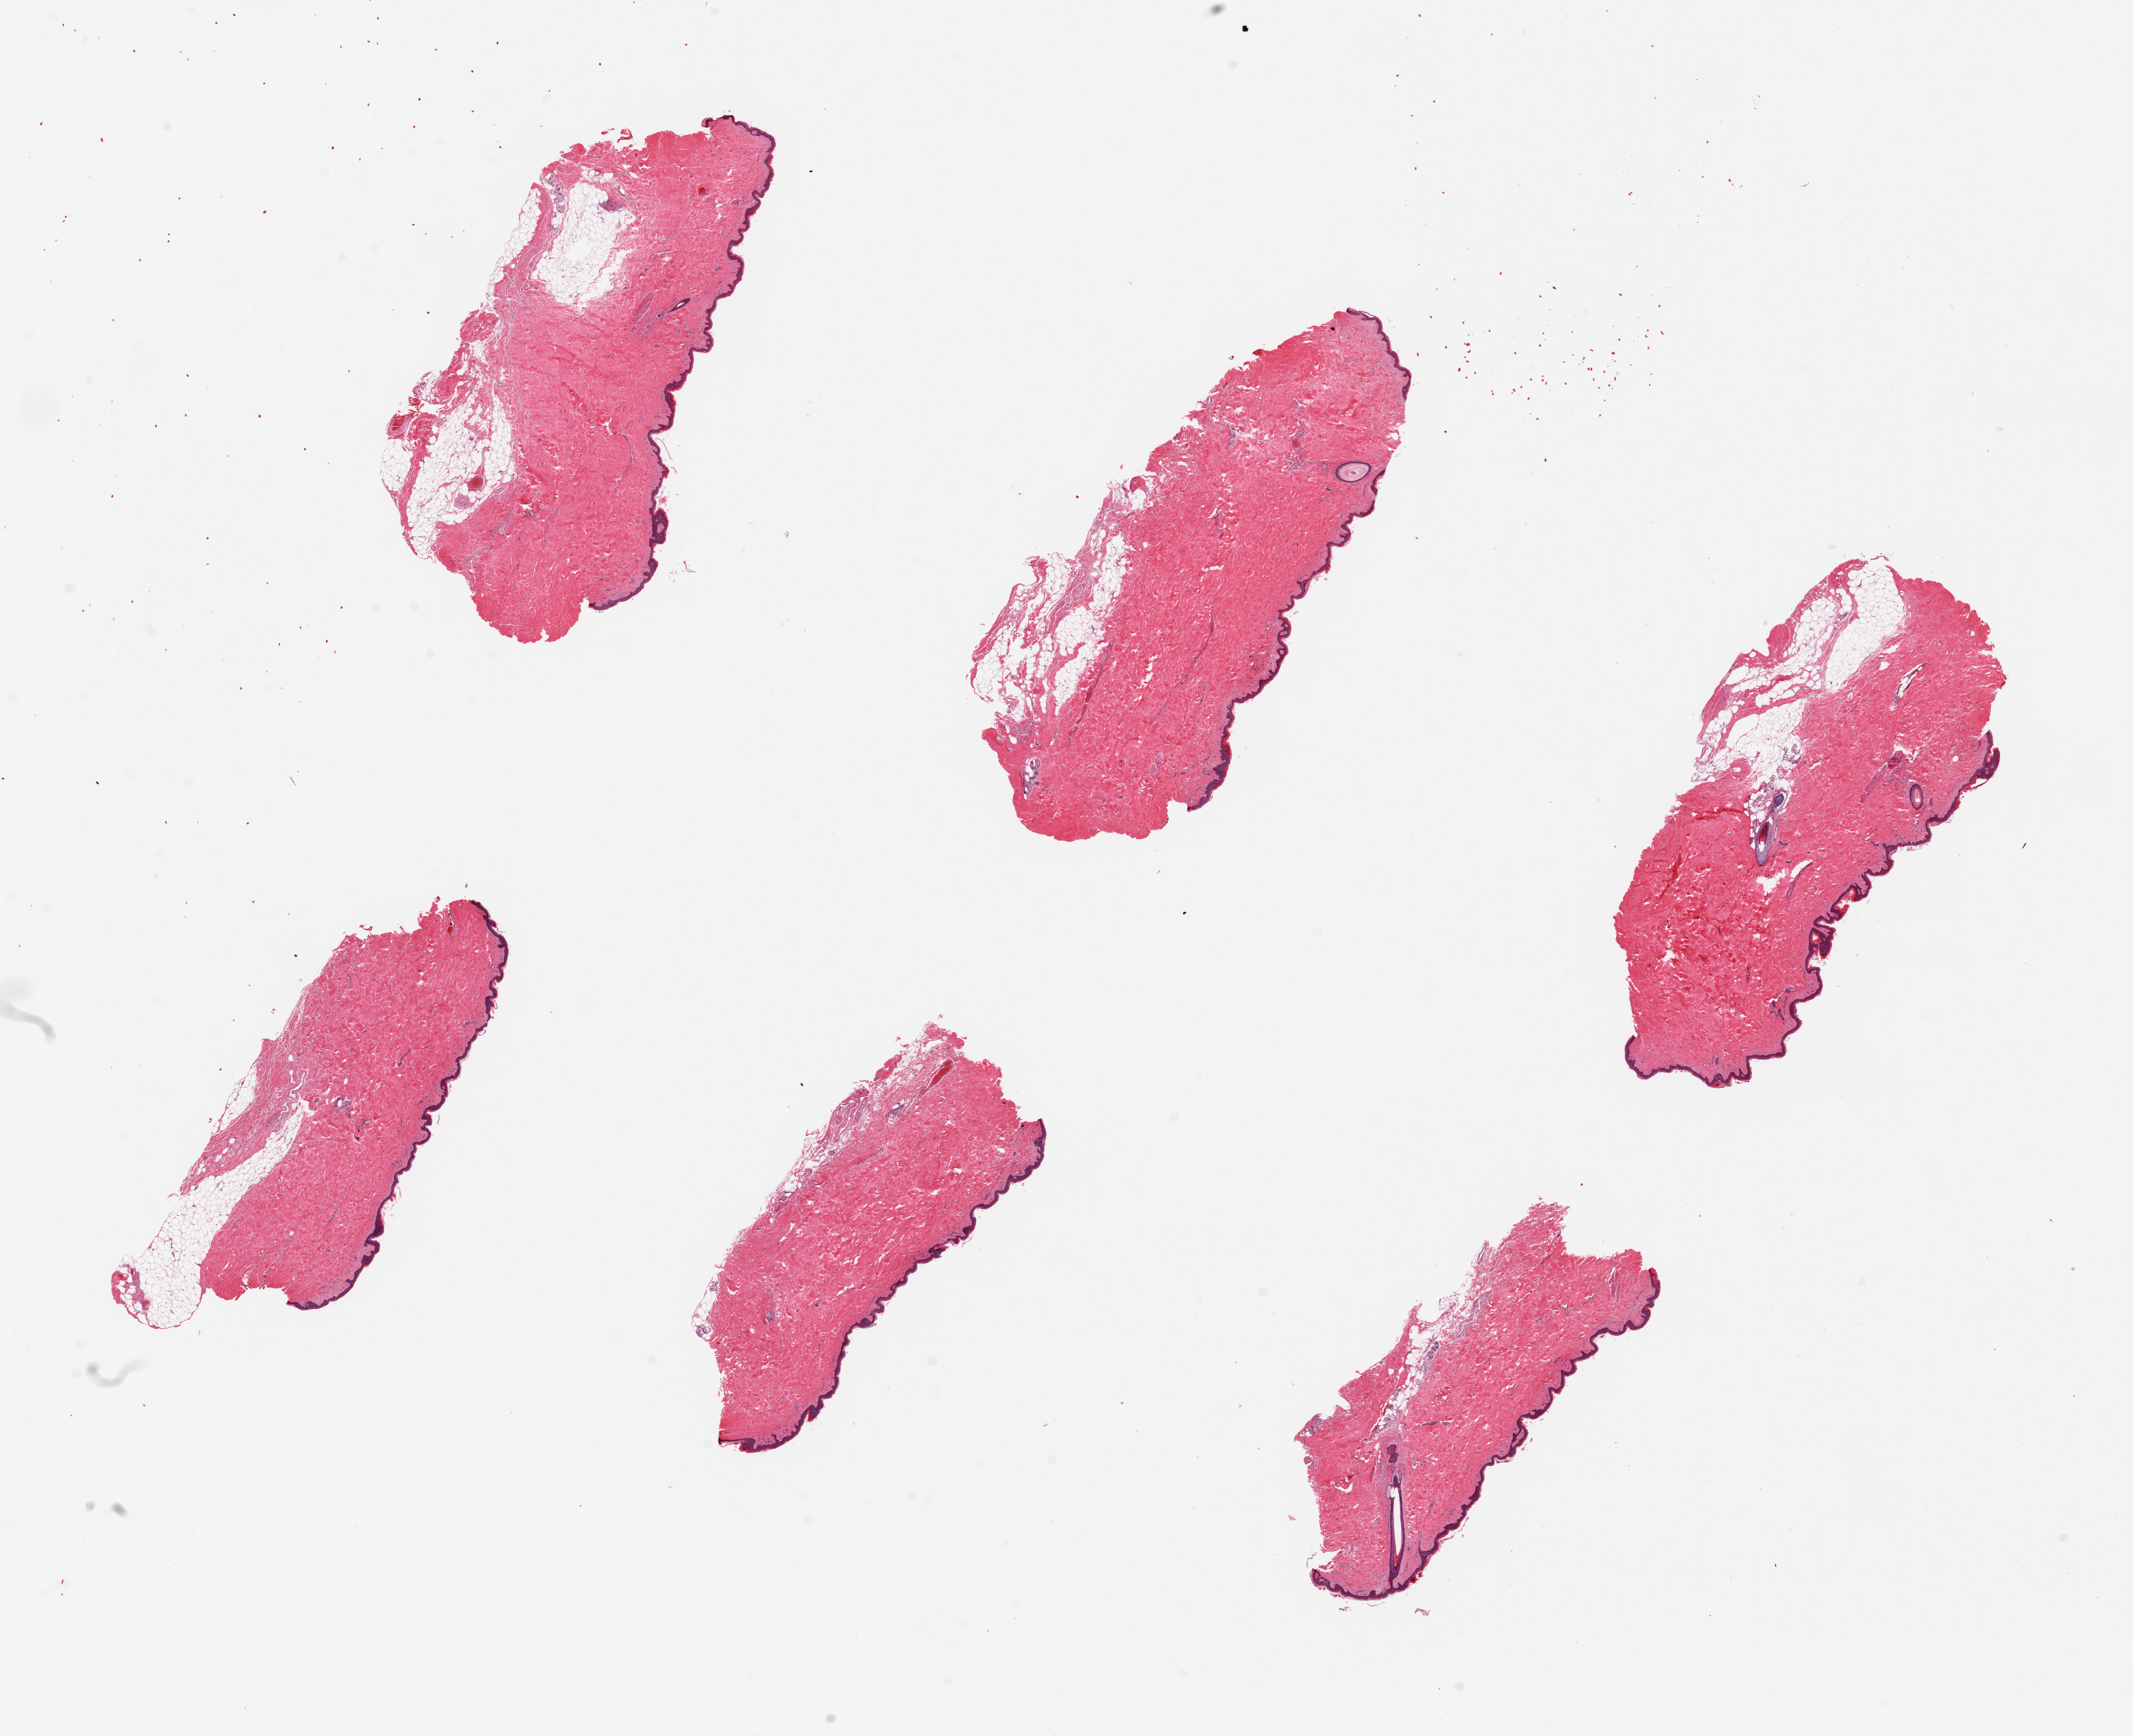
Digitized haematoxylin and eosin-stained section, brightfield — shown as a low-resolution overview of the whole scanned area (about 24.6 x 20.0 mm, slide scanned at 20x). PAXgene-fixed paraffin-embedded (PFPE) section. Section of skin of suprapubic region (target tissue). Tissue donor sample. Donor sex: female.
Pathologist's review note for this sample: 6 pieces. up to 7x3mm; up to 1 mm subcutaneous adipose.